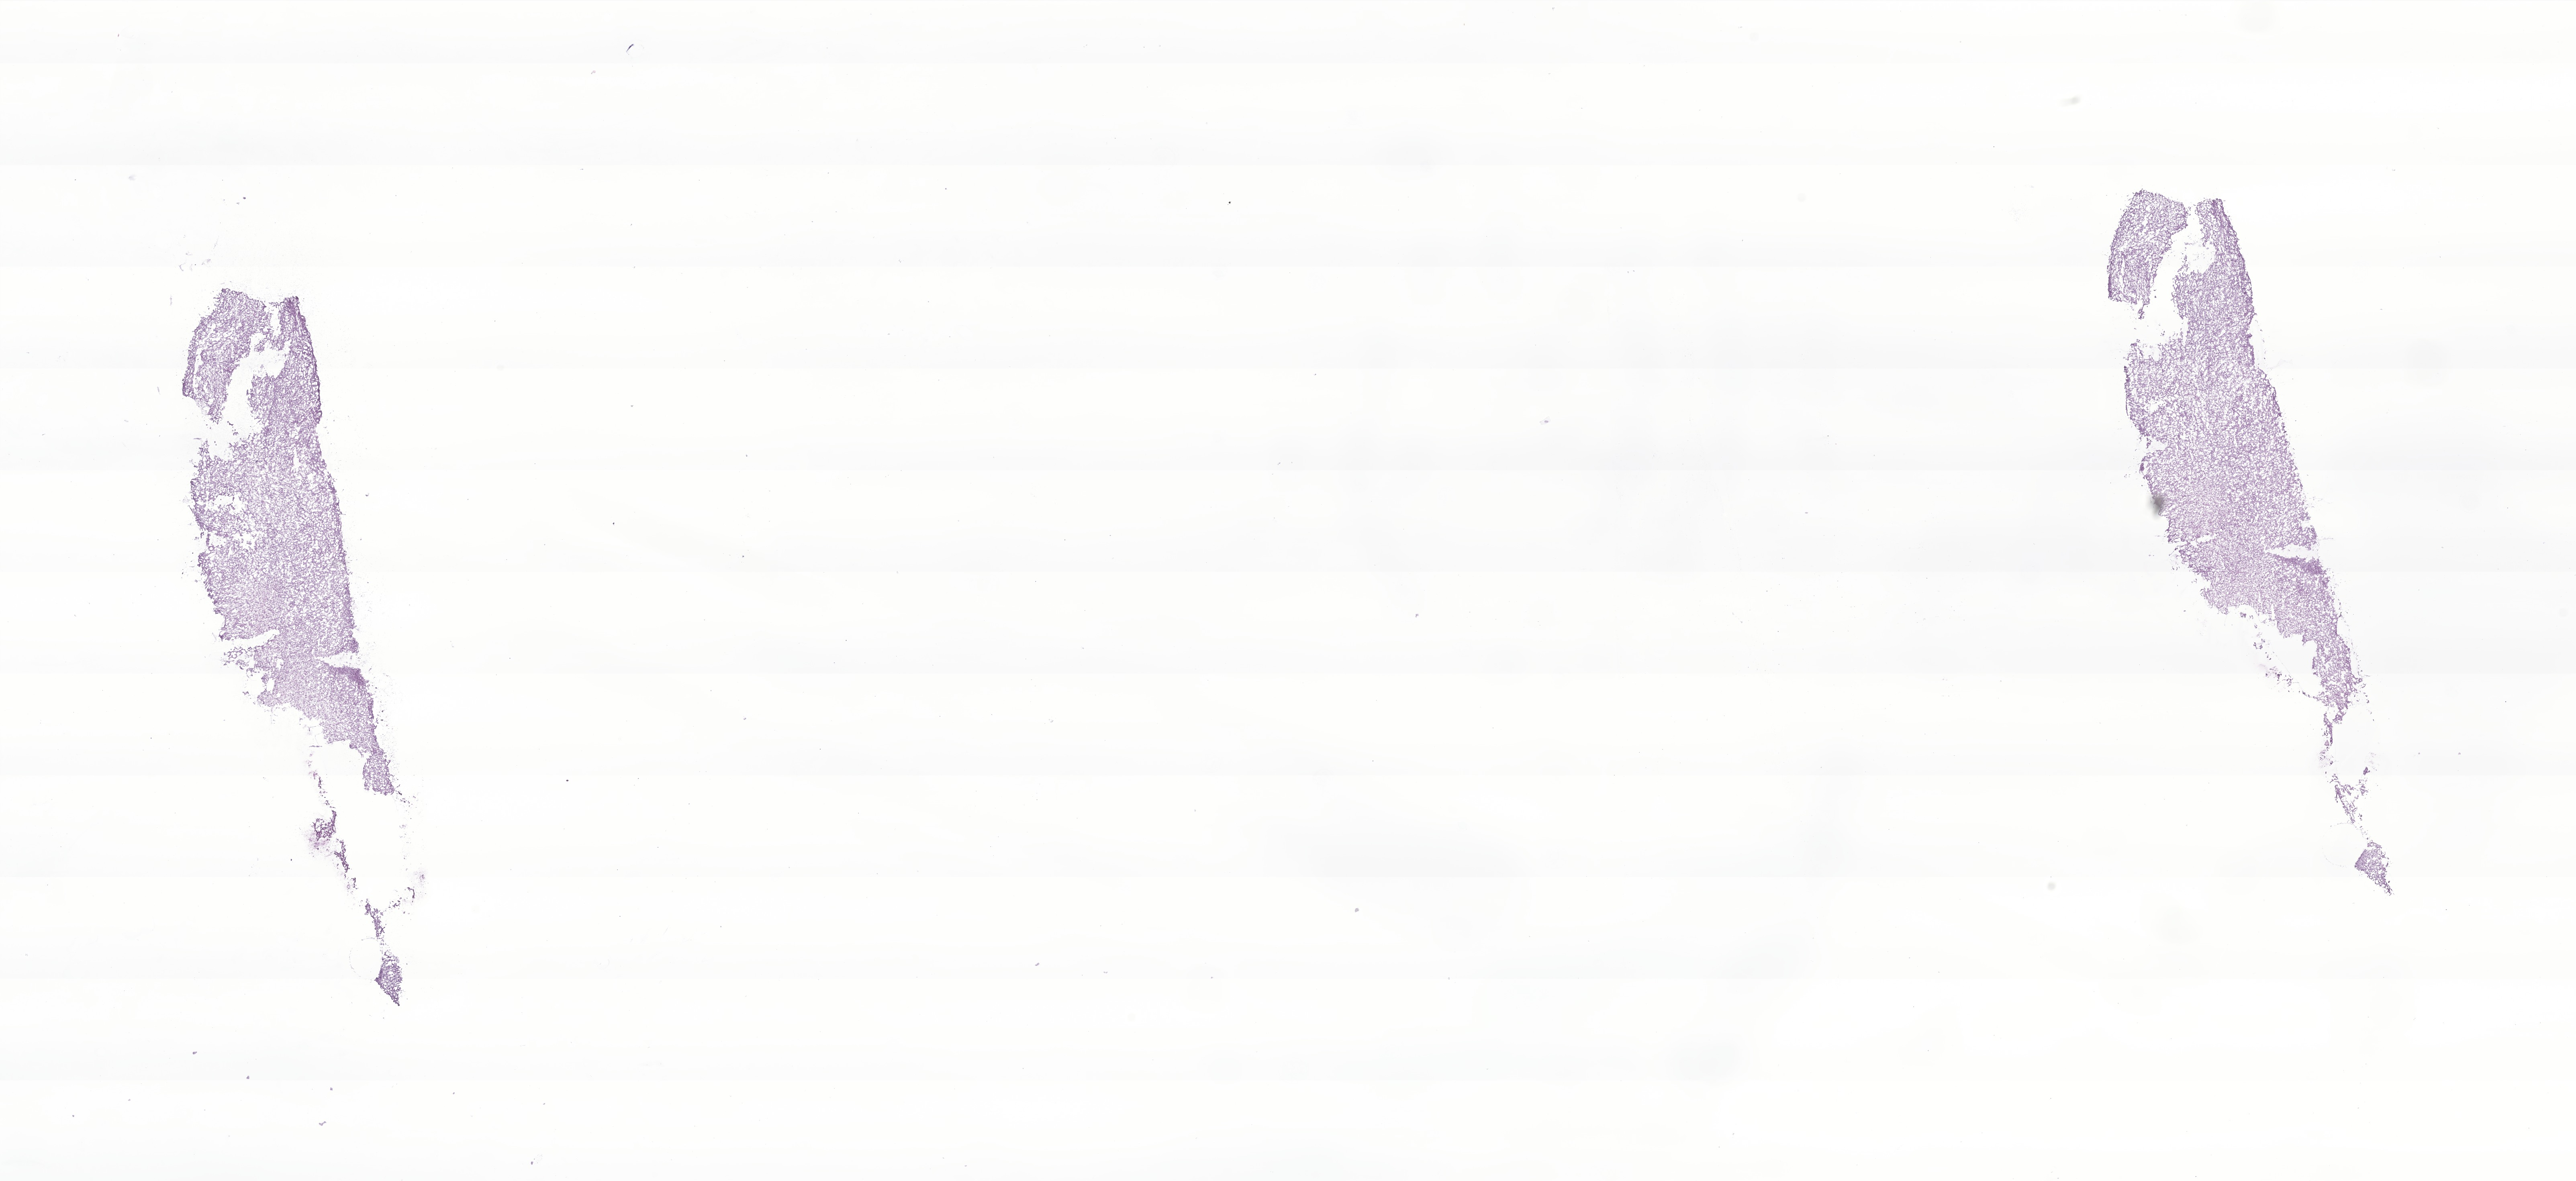
Digitized hematoxylin and eosin (H&E)-stained section of tumor tissue from the ovary, a low-resolution overview of the entire scanned area, about 27.0 x 12.4 mm, frozen section. Patient: female, age 149 months (12 years 5 months).
Recorded diagnosis: Adult granulosa cell tumor of ovary.